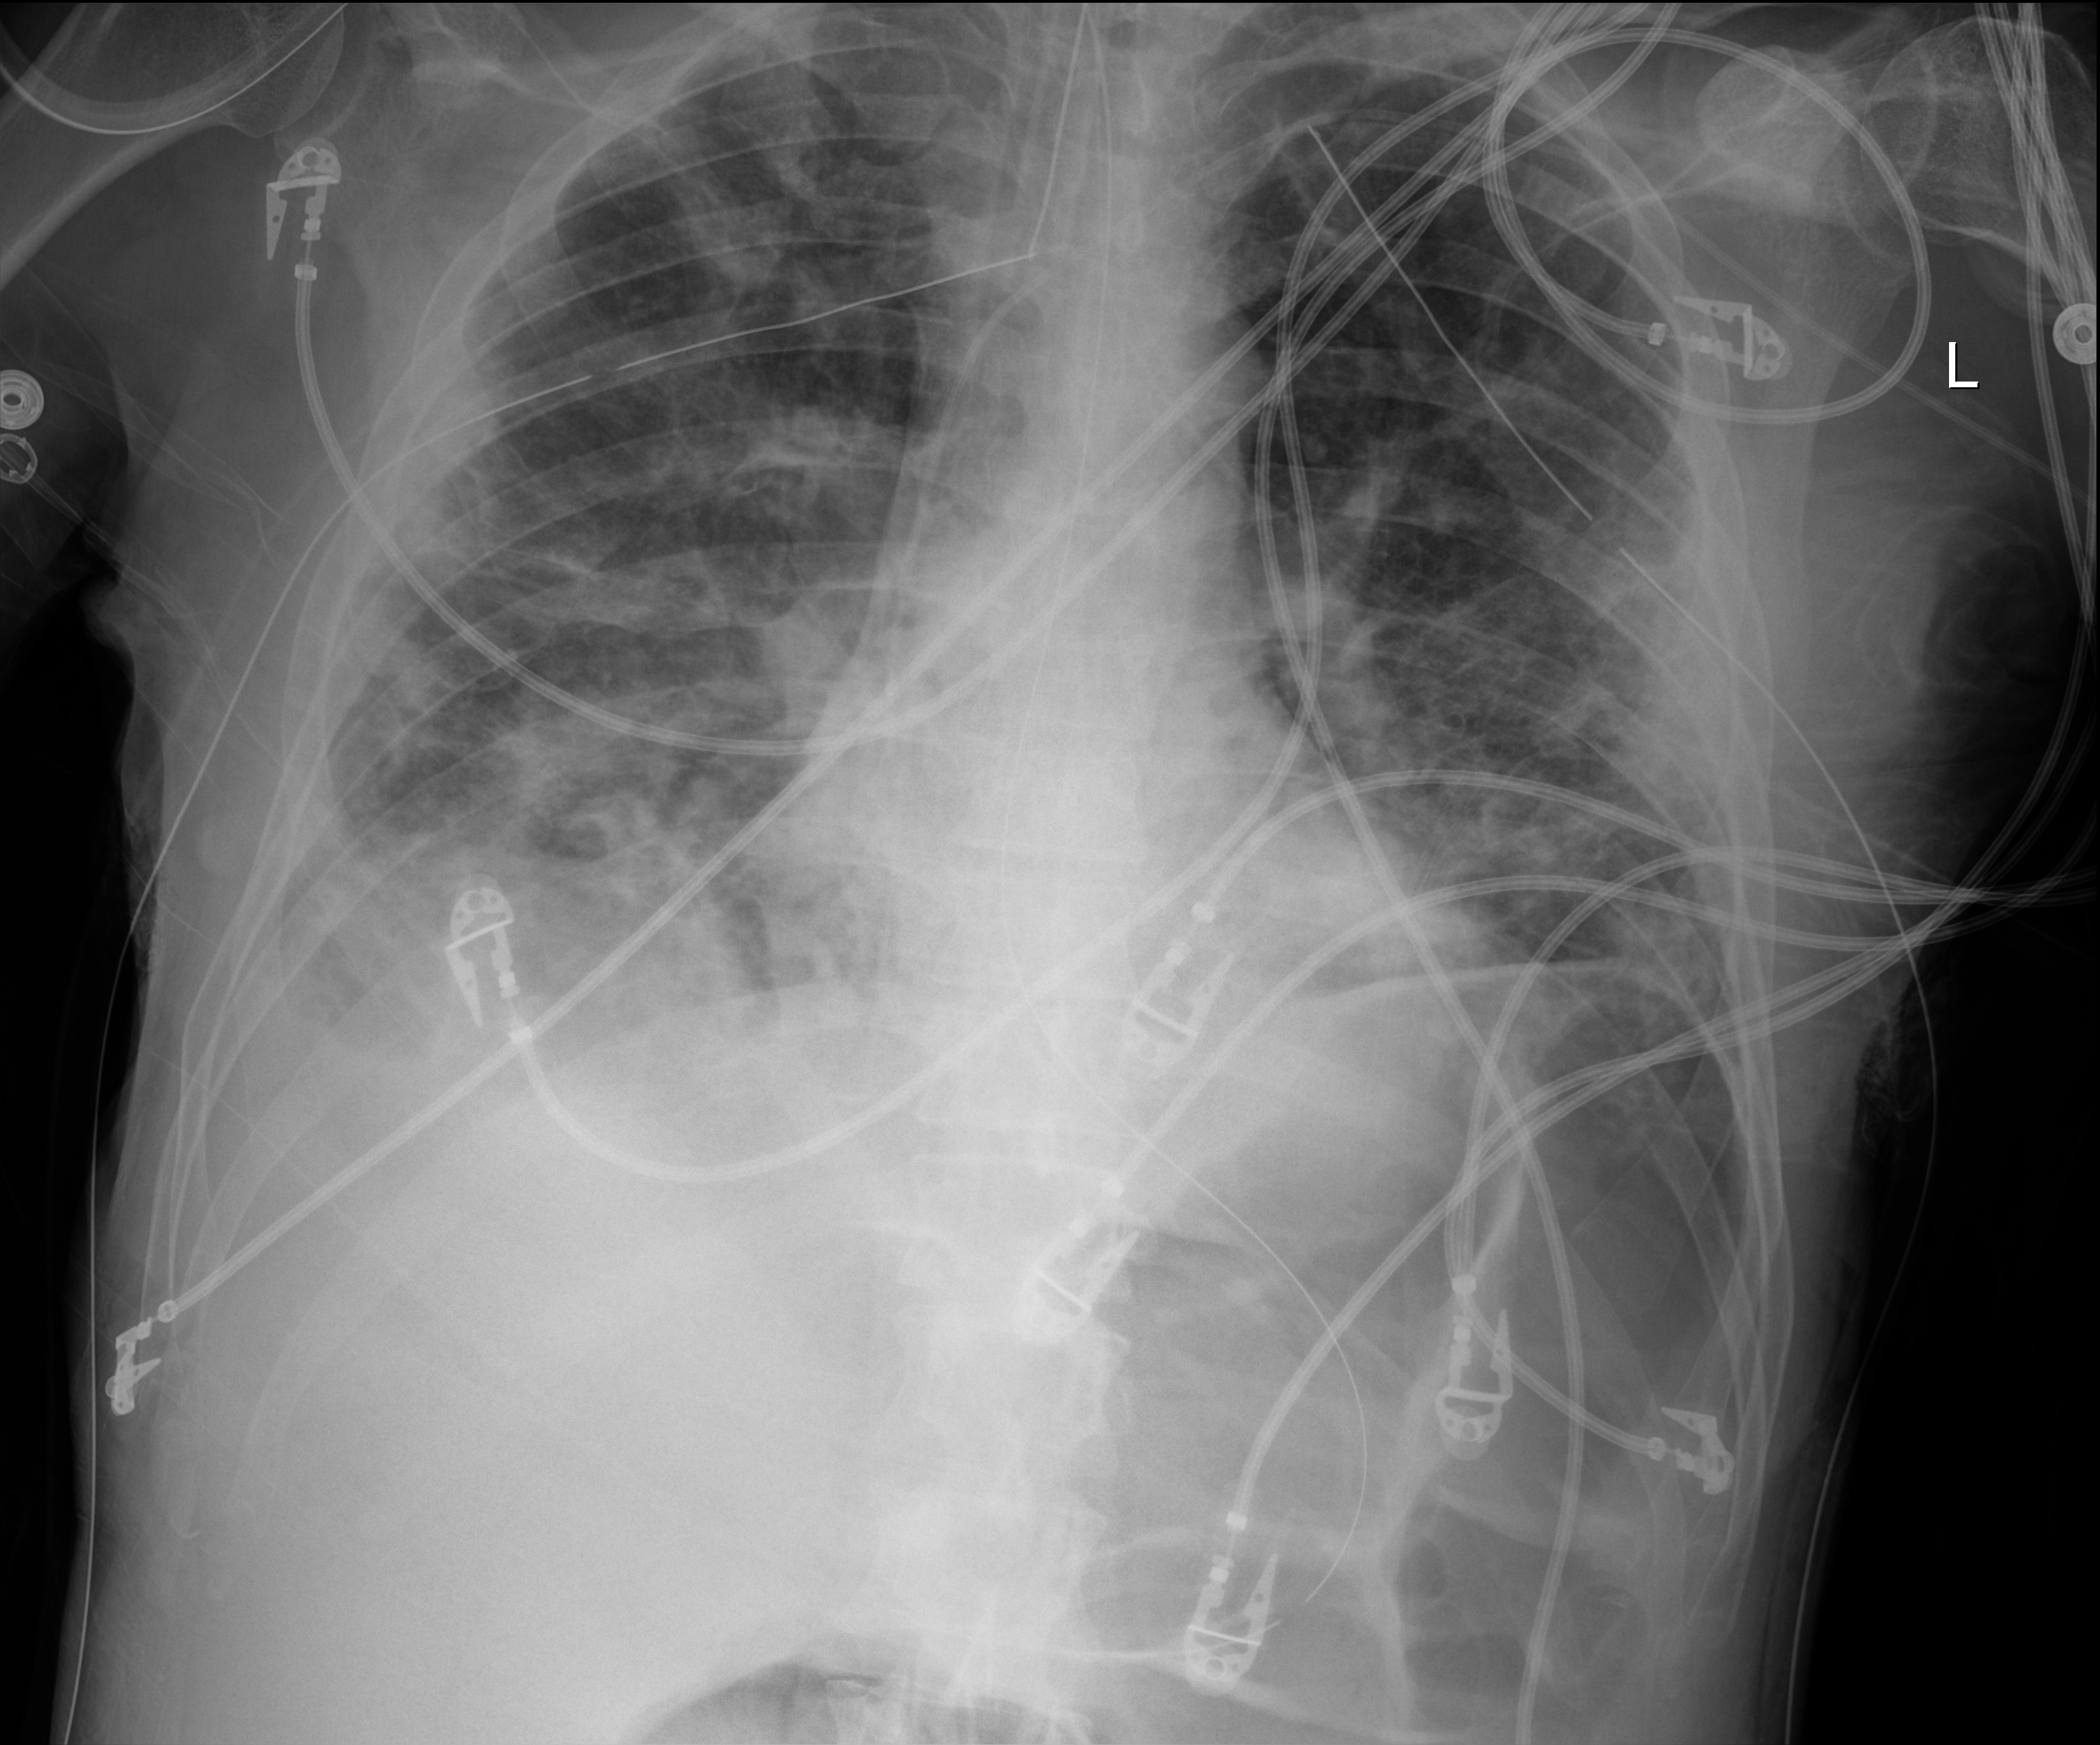
Portable chest radiograph; anteroposterior (AP) projection. Male patient hospitalised with COVID-19, age 18–59 years.
Hospital-stay facts (about this admission, not read from this image; timing relative to this image not recorded):
- admitted to intensive care during this hospital stay: yes
- length of hospital stay: 96 days
- mechanically ventilated during this hospital stay: yes